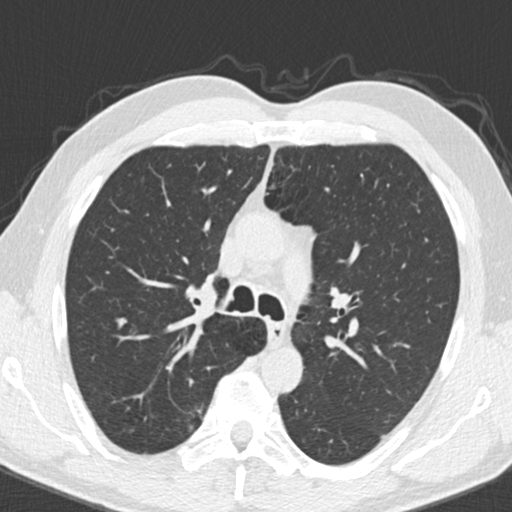
Chest CT (low-dose screening protocol), one axial image, third screening round (two years after baseline), lung window (W 1500 / L -600 HU), slice 60 of 192 in the series. Male participant, aged 55 years at enrolment. Current smoker at enrolment.
Lesion marked by an expert reader, box from (x=172, y=400) to (x=216, y=439) px. Screening reader's record for this exam (one nodule recorded; not confirmed to be the boxed lesion): non-calcified nodule or mass ≥4 mm, right upper lobe, 9 × 7 mm, smooth margins, soft tissue attenuation, pre-existing on the prior screen: no. Participant outcome: lung cancer diagnosed 221 days after this screen — adenocarcinoma, NOS, right upper lobe, poorly differentiated (G3), stage IA (AJCC 6th edition), 15 mm at pathology.